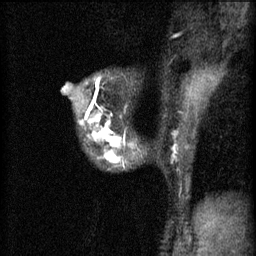
Breast MRI (dynamic contrast-enhanced), one sagittal slice; position 42 of 60 along the scan axis; 3 images stored at this slice position (order not interpretable as contrast timing); 1.5 T; TE 4.2 ms, TR 11 ms; 2 mm slice thickness; 256 × 256 image matrix, field of view 180 × 180 mm. Patient: female, 37 years.
Structures marked on this image (semi-automatic segmentation, software-assisted and operator-edited):
- analysis volume of interest (the breast-tissue region the enhancement analysis was run in; not a lesion): box from (x=78, y=118) to (x=176, y=171) px
- tumour enhancement mask (voxels above the 70 % enhancement threshold inside the analysis volume of interest): (x=79, y=118)–(x=175, y=165)